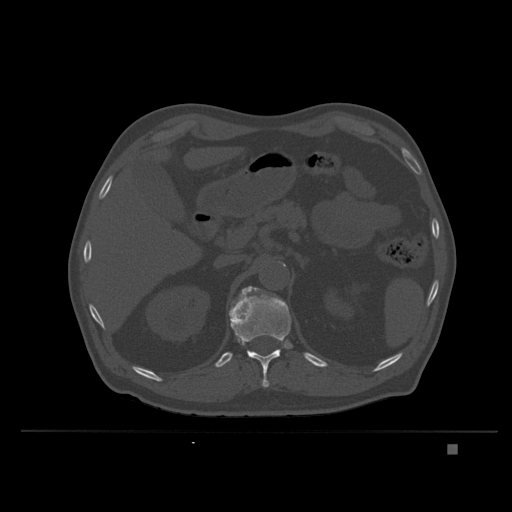
CT including the spine, one axial slice; position 156 of 435 along the scan axis; bone window (W 1800 / L 400 HU); 1.5 mm slice thickness; 512 × 512 image matrix, field of view 434 × 434 mm. Male patient, age 73 years. From the clinical record (not read from this slice): primary cancer: skin.
Outlined on this slice (semi-automatic segmentation, software-assisted and operator-edited):
- T12 vertebra: bounding box (x1, y1, x2, y2) in pixels: (229, 293, 291, 388)